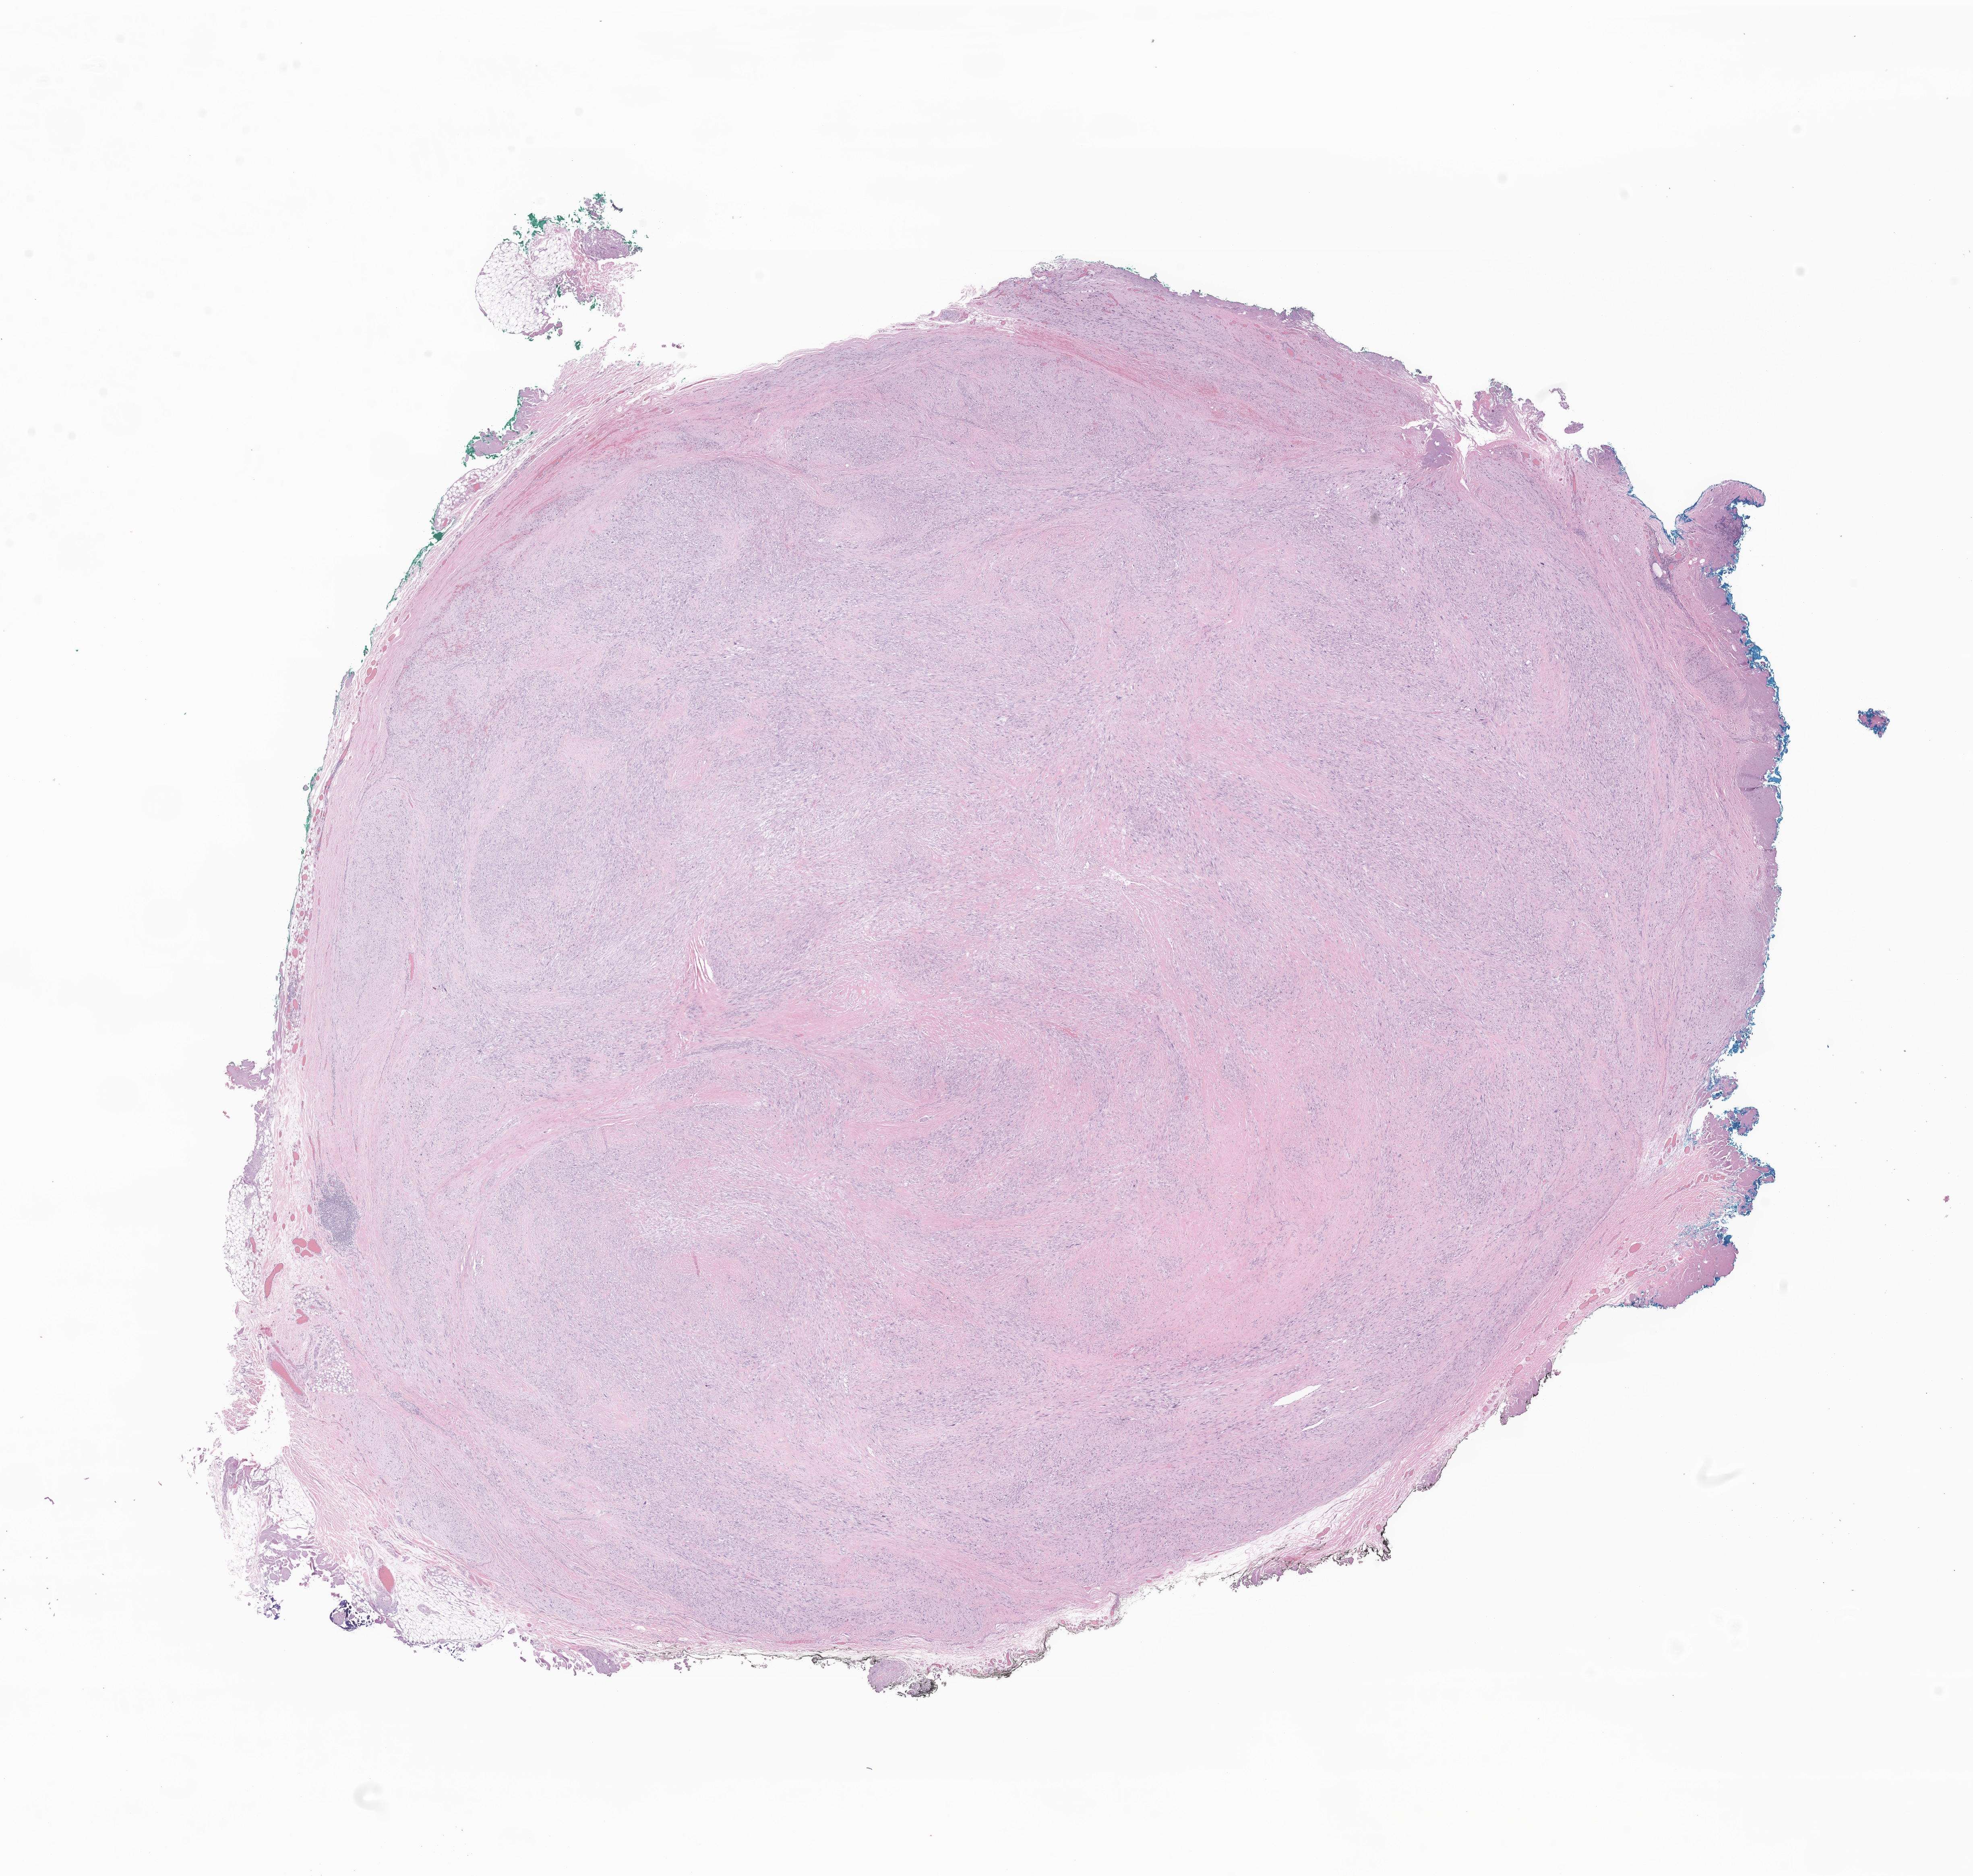
Digitized H&E-stained section of tumor tissue from the soft tissue, a low-resolution overview of the entire scanned area, about 20.7 x 19.6 mm; FFPE section. Patient: female, age 528 days (about 1.4 years).
Diagnosis (ICD-O-3 morphology term): Spindle cell sarcoma.